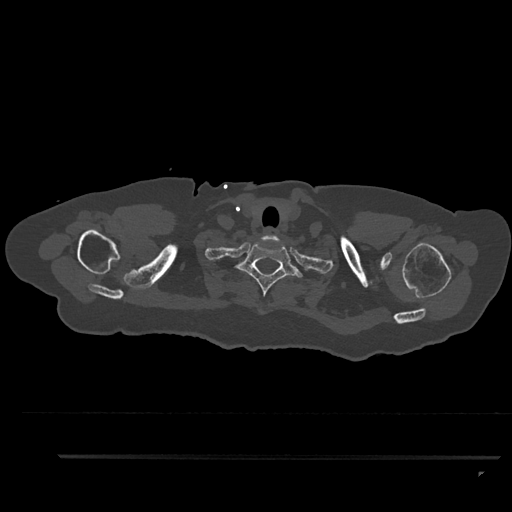
CT including the spine, one axial slice. Slice 763 of 797 in the series (ordered by position). 120 kVp. Bone window (W 1800 / L 400 HU). 0.5 mm slice thickness. 512 × 512 image matrix. Female patient, age 44 years. Case-level facts recorded for this patient, not image findings: primary cancer: renal; vertebrae with lytic lesions (as recorded): L1.
Annotated regions visible in this slice (semi-automatic segmentation, software-assisted and operator-edited):
- T1 vertebra: box from (x=235, y=244) to (x=307, y=297) px